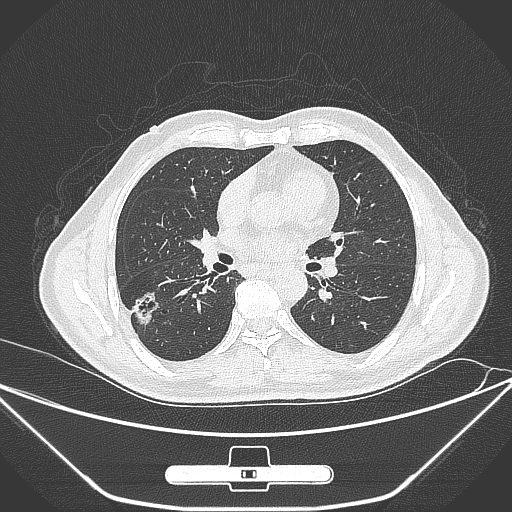
Chest CT, one axial slice; lung window (W 1500 / L -600 HU); 1 mm slice thickness; 512 × 512 image matrix. Male patient, age 71 years. Case-level facts recorded for this patient, not image findings: clinical TNM (as recorded): T1c N0 M0.
Structures marked on this image (rectangle marked by the reading radiologist):
- lung tumour (recorded histology: adenocarcinoma): bounding box (x1, y1, x2, y2) in pixels: (129, 289, 160, 322)